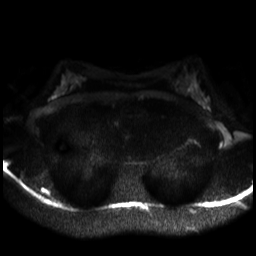
Breast MRI, one axial slice. Position 18 of 30 along the scan axis. Diffusion-weighted series; image 2 of 4 stored at this slice position (different b-values; order by instance number). 3 T. 4 mm slice thickness. 256 × 256 image matrix, field of view 320 × 320 mm. Female patient.
Structures marked on this image (expert manual segmentation):
- tumour on diffusion-weighted imaging: box from (x=206, y=98) to (x=210, y=101) px